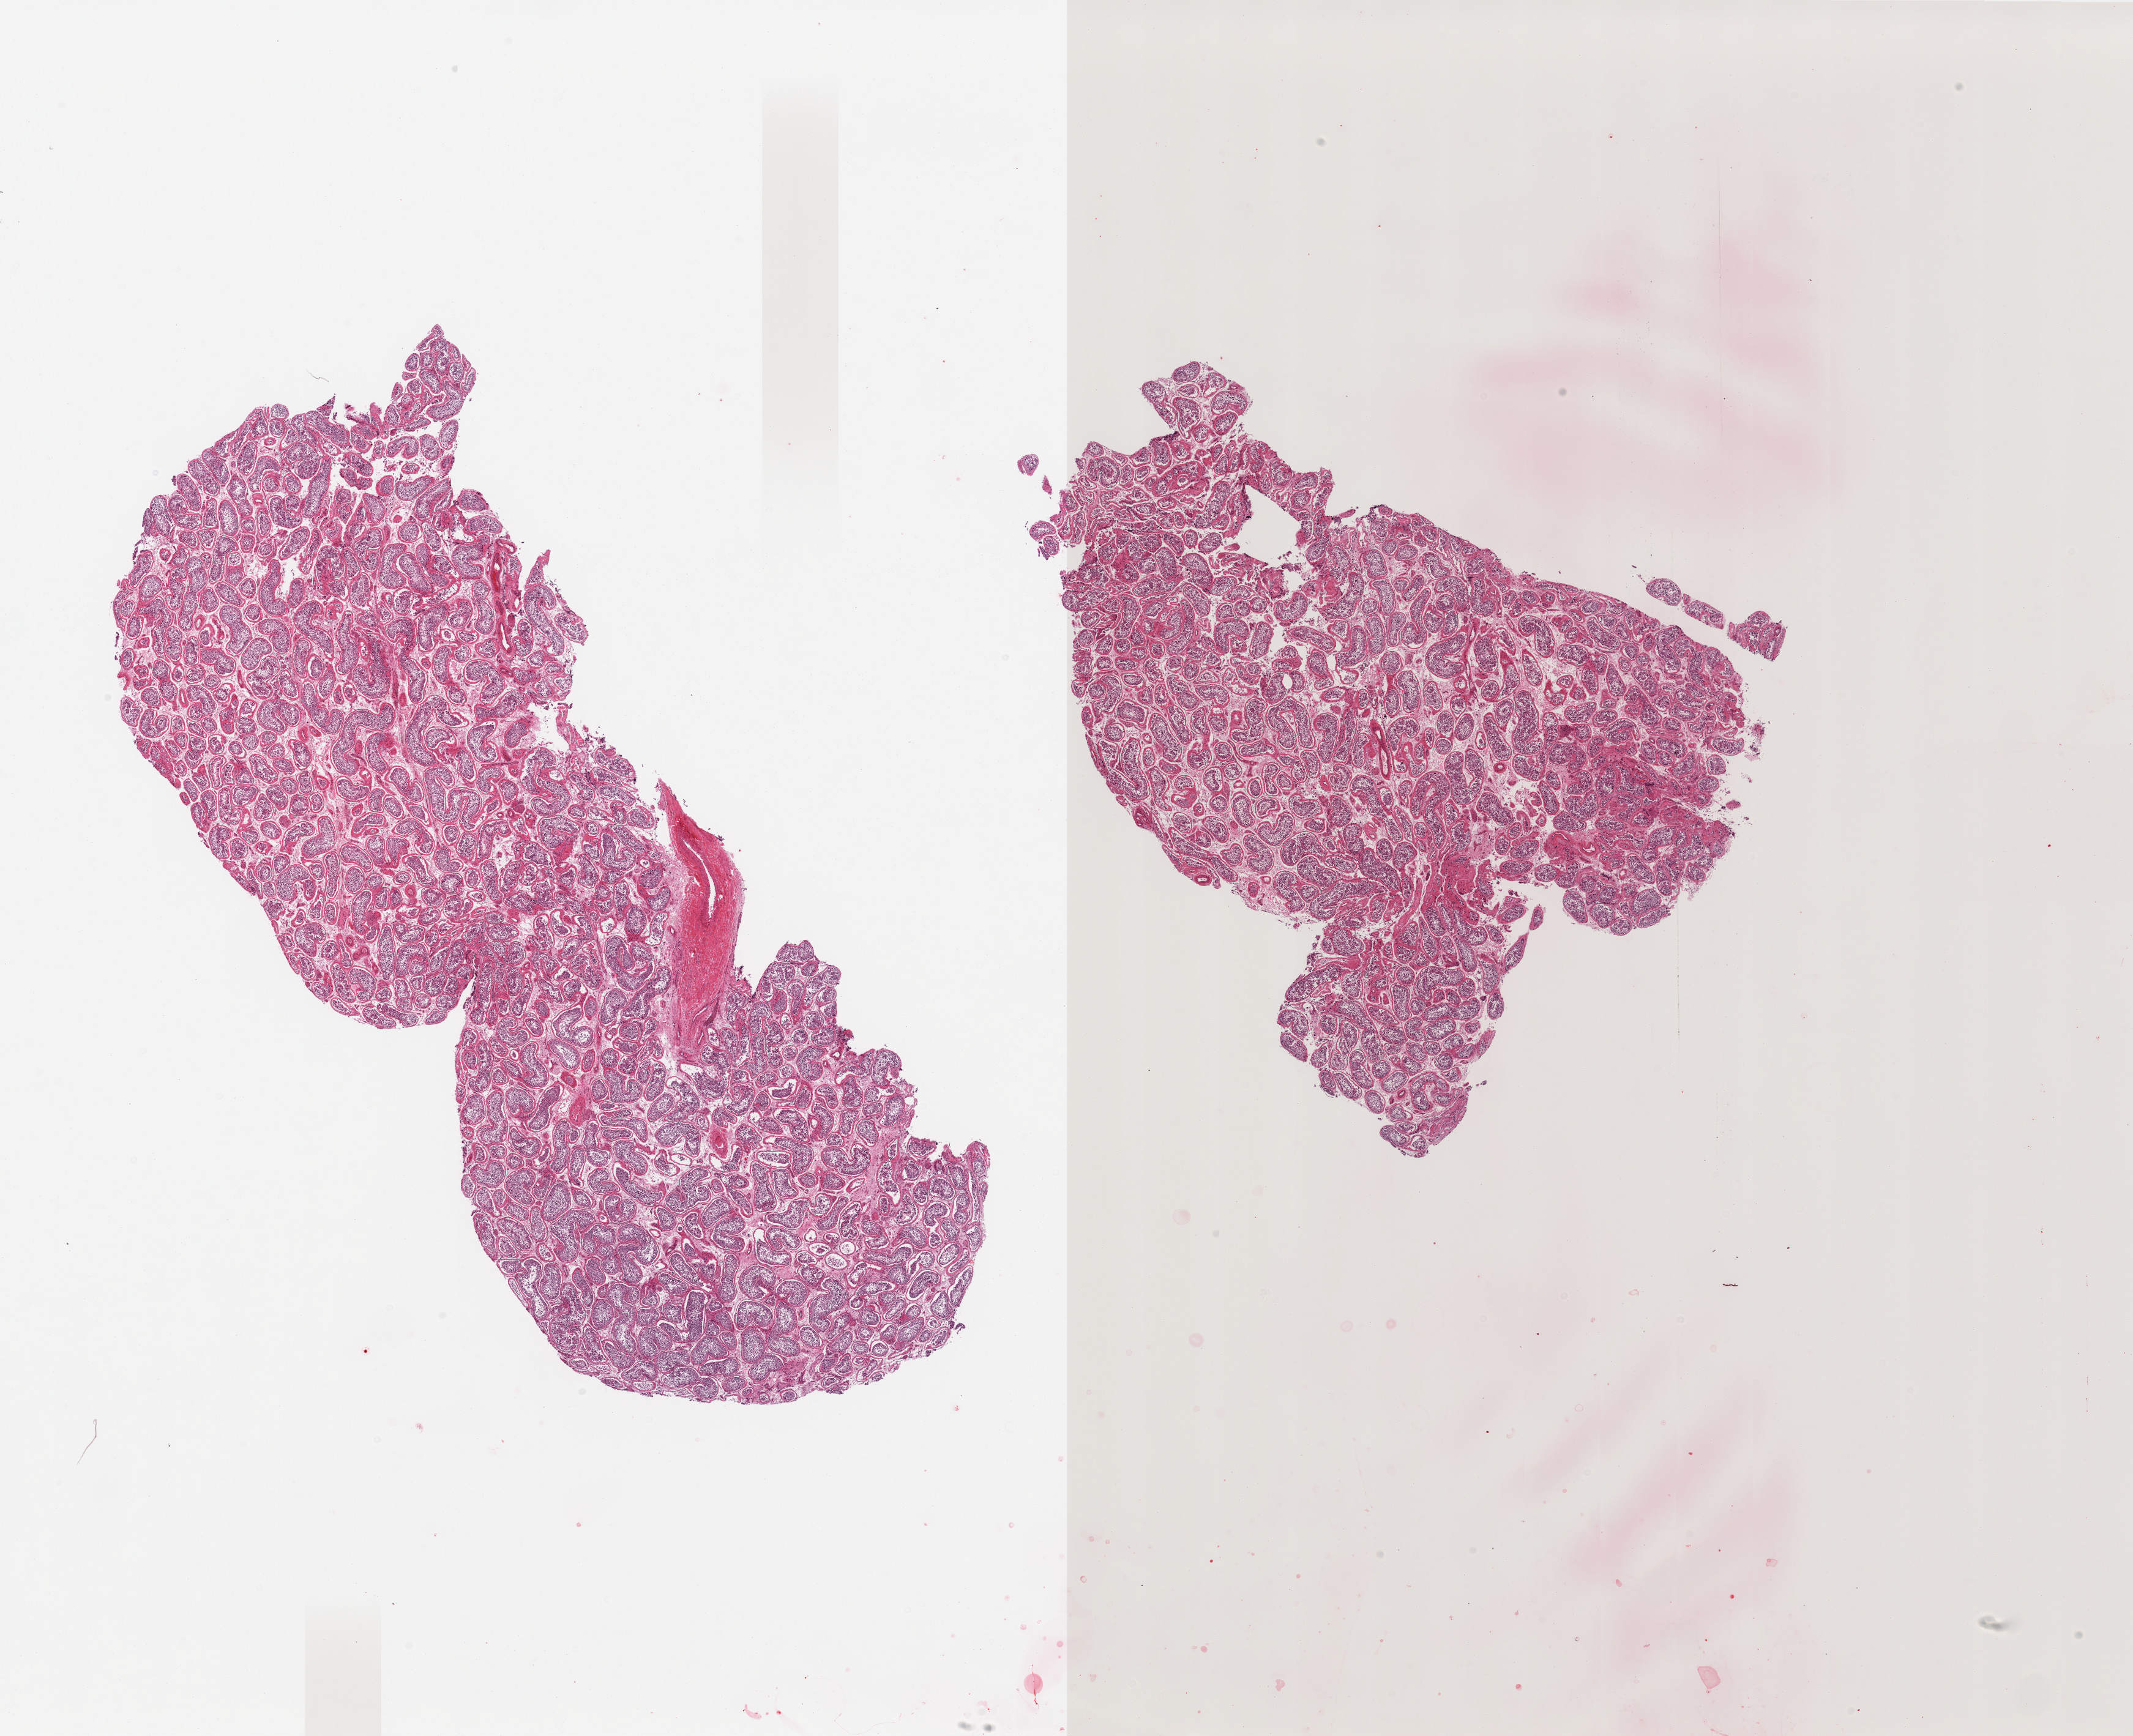
H&E whole-slide image, a low-resolution overview of the entire scanned area, about 27.6 x 22.4 mm (acquisition: 20x scan). PAXgene-fixed paraffin-embedded (PFPE) section. Sampled site (target tissue): testis. Donor tissue sample.
Review note (as recorded): 2 pieces; spermatogenesis present.